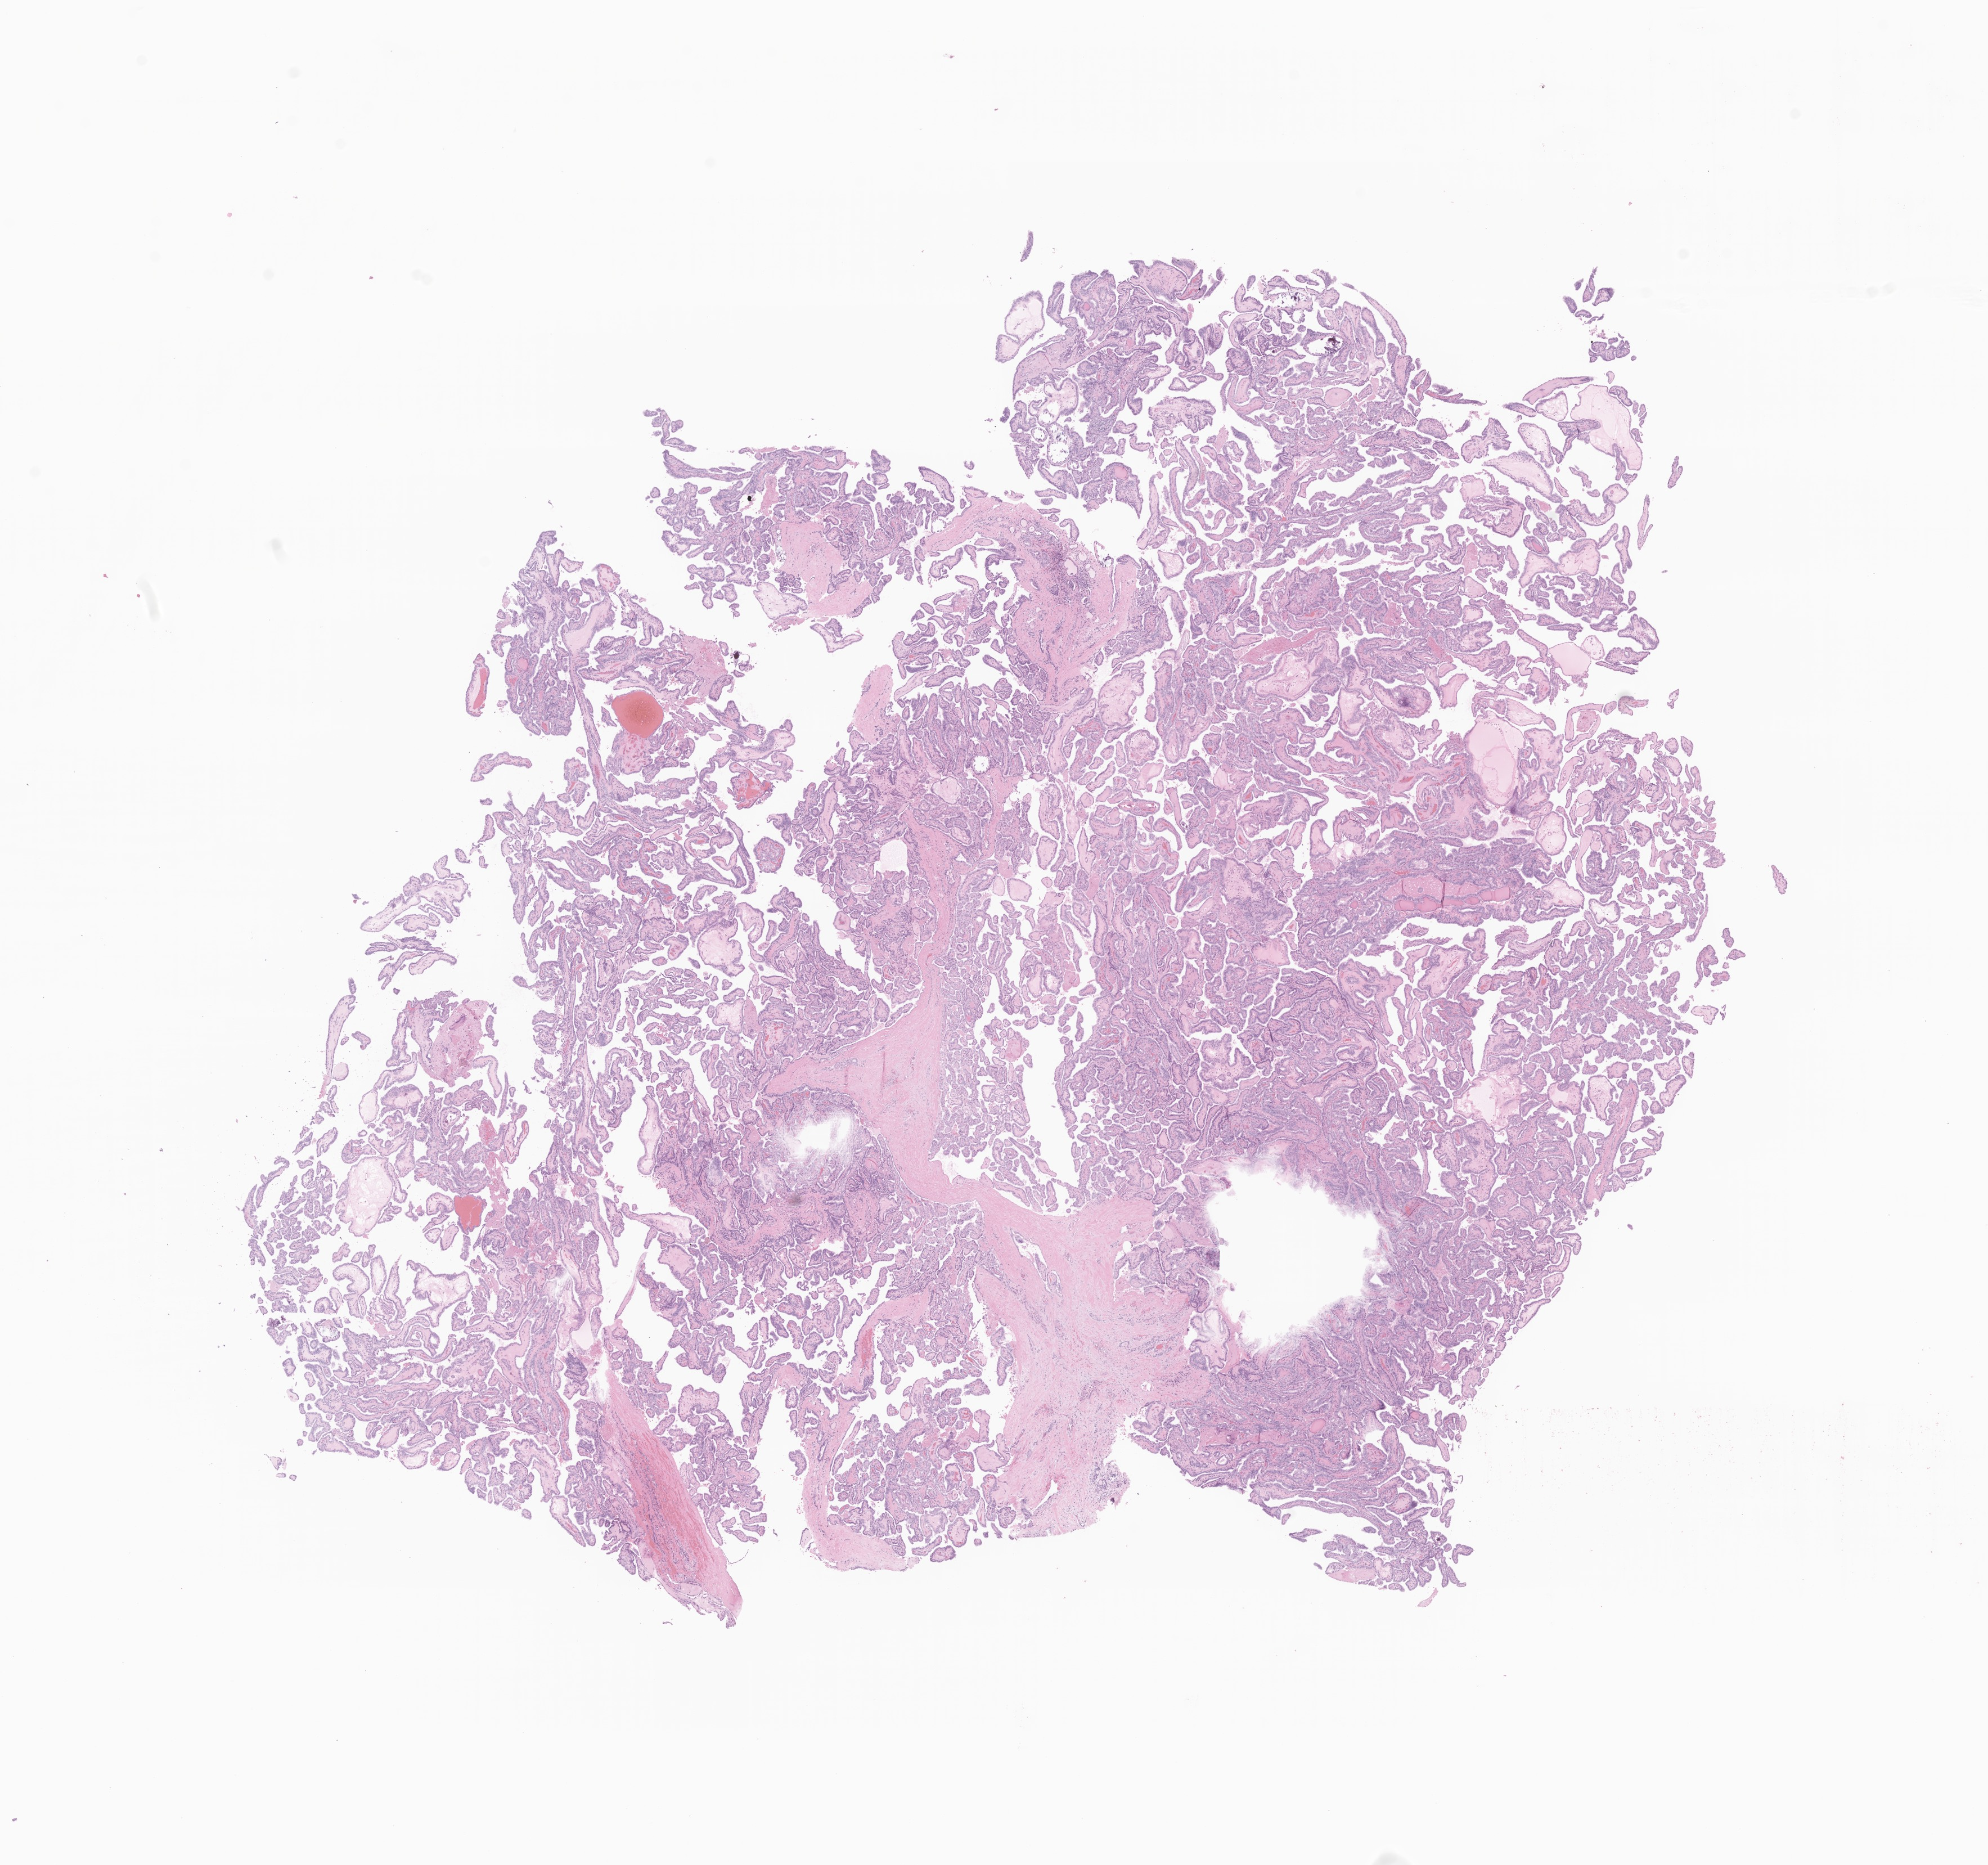
Whole-slide image, haematoxylin and eosin stain of tumor tissue from the thyroid — low-resolution overview of the scanned area, about 14.9 x 14.0 mm, formalin-fixed, paraffin-embedded (FFPE) tissue. Female patient, age 196 months (16 years 4 months).
* diagnosis (ICD-O-3 morphology term): Papillary carcinoma, NOS